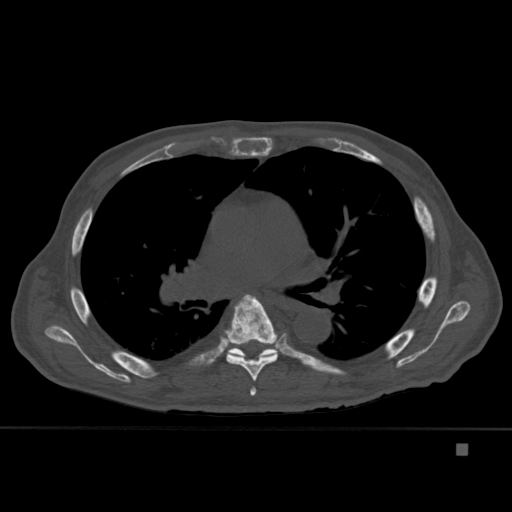
CT including the spine, one axial slice; slice 291 of 451 in the series (ordered by position); bone window (W 1800 / L 400 HU); 1.5 mm slice thickness; 512 × 512 image matrix, field of view 378 × 378 mm. Male patient, age 75 years. Case-level facts recorded for this patient, not image findings: primary cancer: prostate.
Structures marked on this image (semi-automatically segmented with operator editing):
- T5 vertebra: bounding box (x1, y1, x2, y2) in pixels: (250, 386, 257, 396)
- T6 vertebra: (224, 294, 279, 381)
- T7 vertebra: (229, 345, 277, 358)